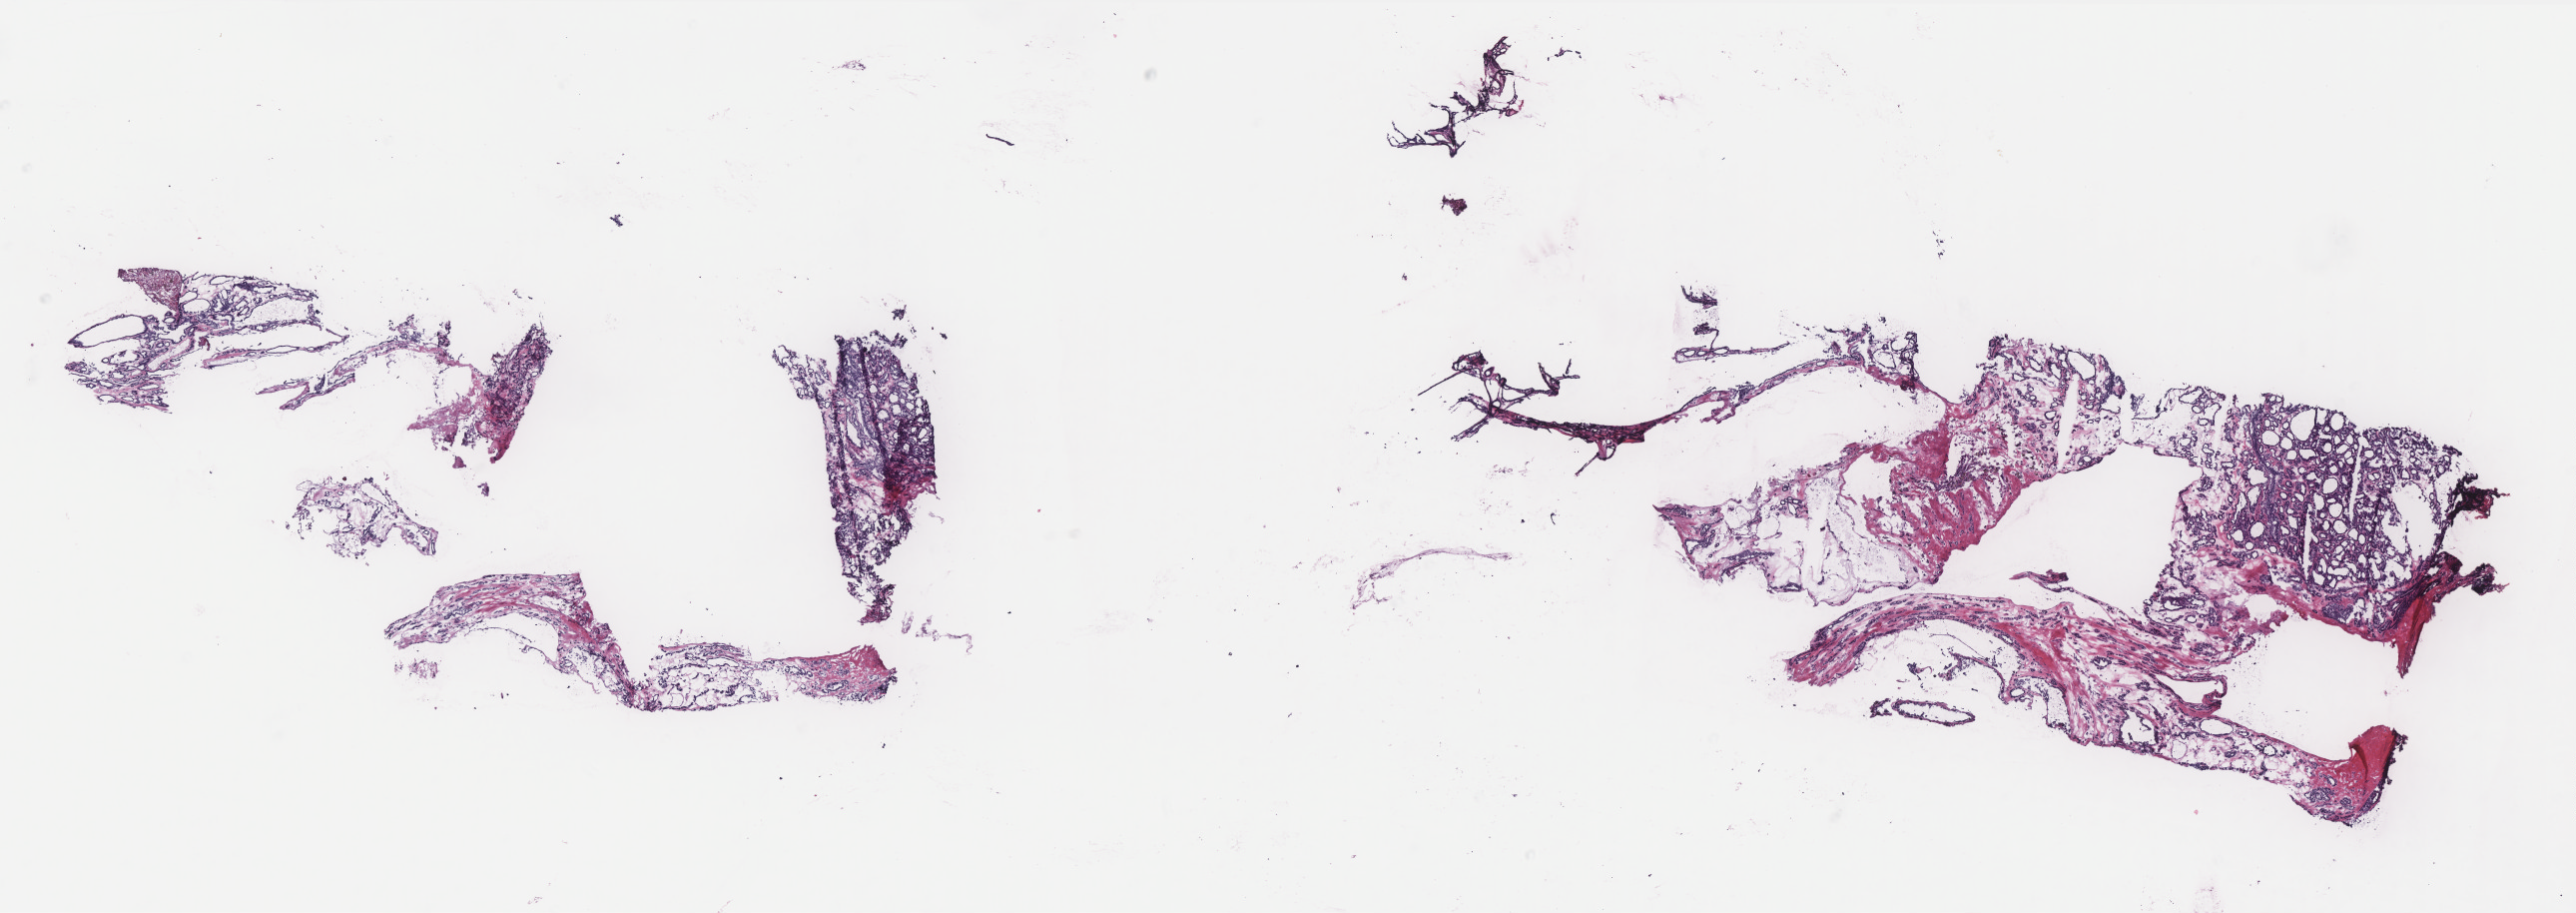
Hematoxylin and eosin (H&E) stained whole-slide image, whole scanned area (about 20.7 x 7.3 mm) shown as a low-resolution overview; frozen section from the top of the tissue portion; thyroid, primary tumour sample. Female patient; age at initial diagnosis 67 years. Slide review estimates, as recorded: tumour cells 70%, tumour nuclei 70%, normal cells 0%, stromal cells 30%, necrosis 0%. Infiltration values recorded for this section: lymphocyte infiltration 2%, monocyte infiltration 1%, neutrophil infiltration 0%.
Histologic diagnosis: Papillary adenocarcinoma, NOS. Laterality: bilateral. AJCC pathologic stage: II (7th edition).